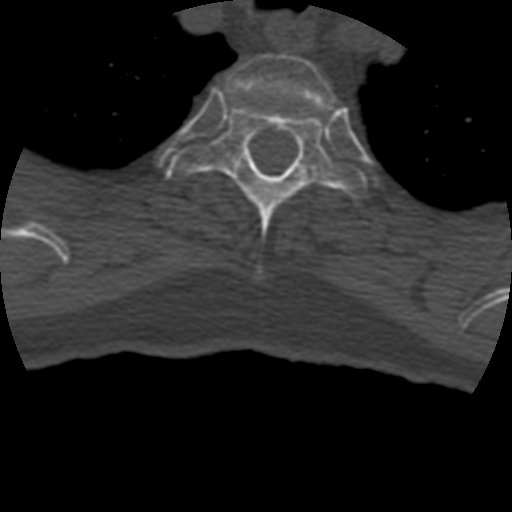
CT including the spine, one axial slice; reconstruction kernel STANDARD; bone window (W 1800 / L 400 HU); 1.25 mm slice thickness; 512 × 512 image matrix. Patient age 69 years. Case-level facts recorded for this patient, not image findings: primary cancer: prostate.
Outlined on this slice (semi-automatic segmentation, software-assisted and operator-edited):
- T2 vertebra: bounding box [x1, y1, x2, y2] px = [227, 54, 336, 109]
- T3 vertebra: [166, 104, 368, 275]